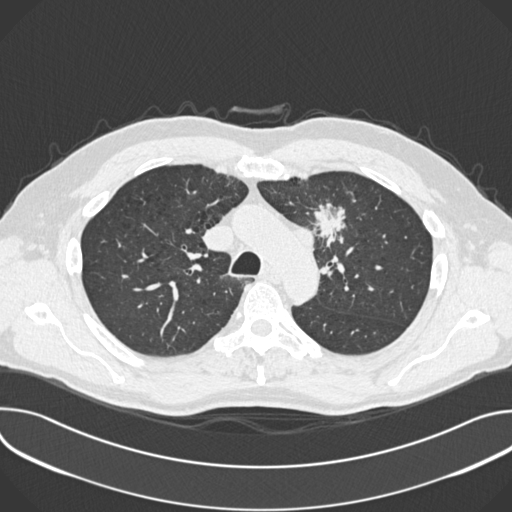
Low-dose screening chest CT, one axial slice; slice 267 of 361 in the series (ordered by position); 120 kVp; lung window (W 1500 / L -600 HU); 1 mm slice thickness; 512 × 512 image matrix, field of view 380 × 380 mm.
Annotated regions visible in this slice (outlined manually by an expert reader):
- lesion 1 (tumor, upper lobe of left lung): bounding box <315,207,345,245> (left, top, right, bottom; pixels)